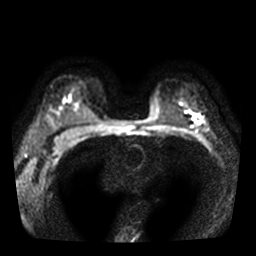
Breast MRI, one axial slice; position 25 of 36 along the scan axis; diffusion-weighted series; image 2 of 4 stored at this slice position (different b-values; order by instance number); 3 T; 5 mm slice thickness; 256 × 256 image matrix, field of view 320 × 320 mm. Female patient.
Annotated regions visible in this slice (outlined manually by an expert reader):
- tumour on diffusion-weighted imaging: bounding box [x1, y1, x2, y2] px = [192, 115, 201, 124]